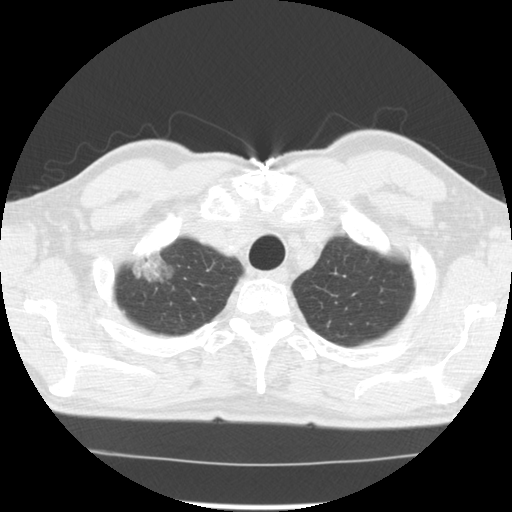
Low-dose screening chest CT, axial slice. Third annual screen. Lung window (W 1500 / L -600 HU). Standard (soft-tissue) reconstruction kernel (STANDARD). Slice 17 of 128 in the series. 512 × 512 image matrix. Male, age 64 years at enrolment. Former smoker at enrolment.
Expert reader's lesion annotation, bounding box <118,238,186,295> (left, top, right, bottom; pixels). The screening reader recorded 3 non-calcified nodules or masses ≥4 mm on this exam (right upper lobe, right lower lobe, left upper lobe); which of them this box marks is not recorded. Lung cancer was diagnosed 30 days after this screen: adenocarcinoma, NOS, right upper lobe, well differentiated (G1), stage IB (AJCC 6th edition), 45 mm at pathology.